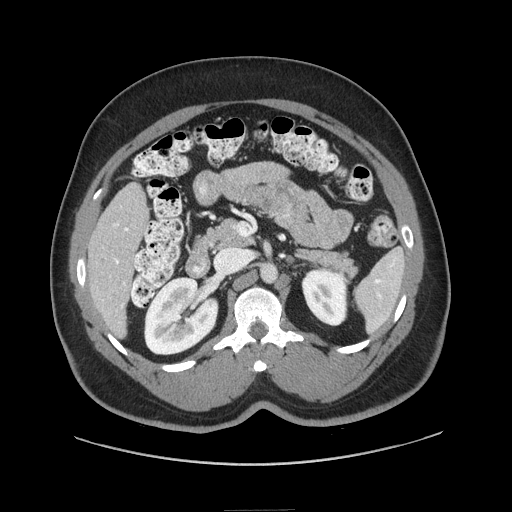
Contrast-enhanced abdominal CT (liver protocol), one axial slice. Slice 30 of 87 in the series (ordered by position). Reconstruction kernel STANDARD. Soft-tissue window (W 400 / L 40 HU). 2.5 mm slice thickness. 512 × 512 image matrix, field of view 440 × 440 mm. Case-level facts recorded for this patient, not image findings: diagnosis: hepatocellular carcinoma (patient treated with transarterial chemoembolisation; whether this scan precedes or follows treatment is not stated here); TNM stage (as recorded): Stage-II; Child-Pugh class: A; tumour differentiation: moderately differentiated.
Annotated regions visible in this slice (semi-automatic segmentation, software-assisted and operator-edited):
- liver parenchyma outside the tumour (the mass and vessels are separate outlines, so this box may not span the whole liver): bounding box <88,182,148,336> (left, top, right, bottom; pixels)
- liver vessels: <113,223,128,307>